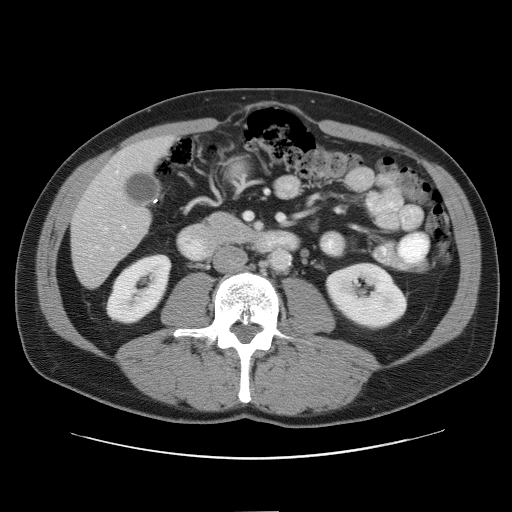
Contrast-enhanced abdominal CT, one axial slice. Position 20 of 52 along the scan axis. Reconstruction kernel STANDARD. 120 kVp. Intravenous contrast given. Soft-tissue window (W 400 / L 40 HU). 5 mm slice thickness. 512 × 512 image matrix. Male patient, age 70 years. From the clinical record (not read from this slice): diagnosis: colorectal cancer liver metastases, imaged before liver resection; multiple liver metastases: yes; largest metastasis: 4 cm; chemotherapy before resection: yes.
Structures marked on this image (manually delineated by an expert):
- hepatic veins: bounding box [x1, y1, x2, y2] px = [89, 223, 115, 256]
- liver: [72, 137, 172, 287]
- planned liver remnant (the part of the liver to remain after resection): [118, 137, 172, 173]
- portal vein (with intrahepatic branches): [115, 164, 127, 230]